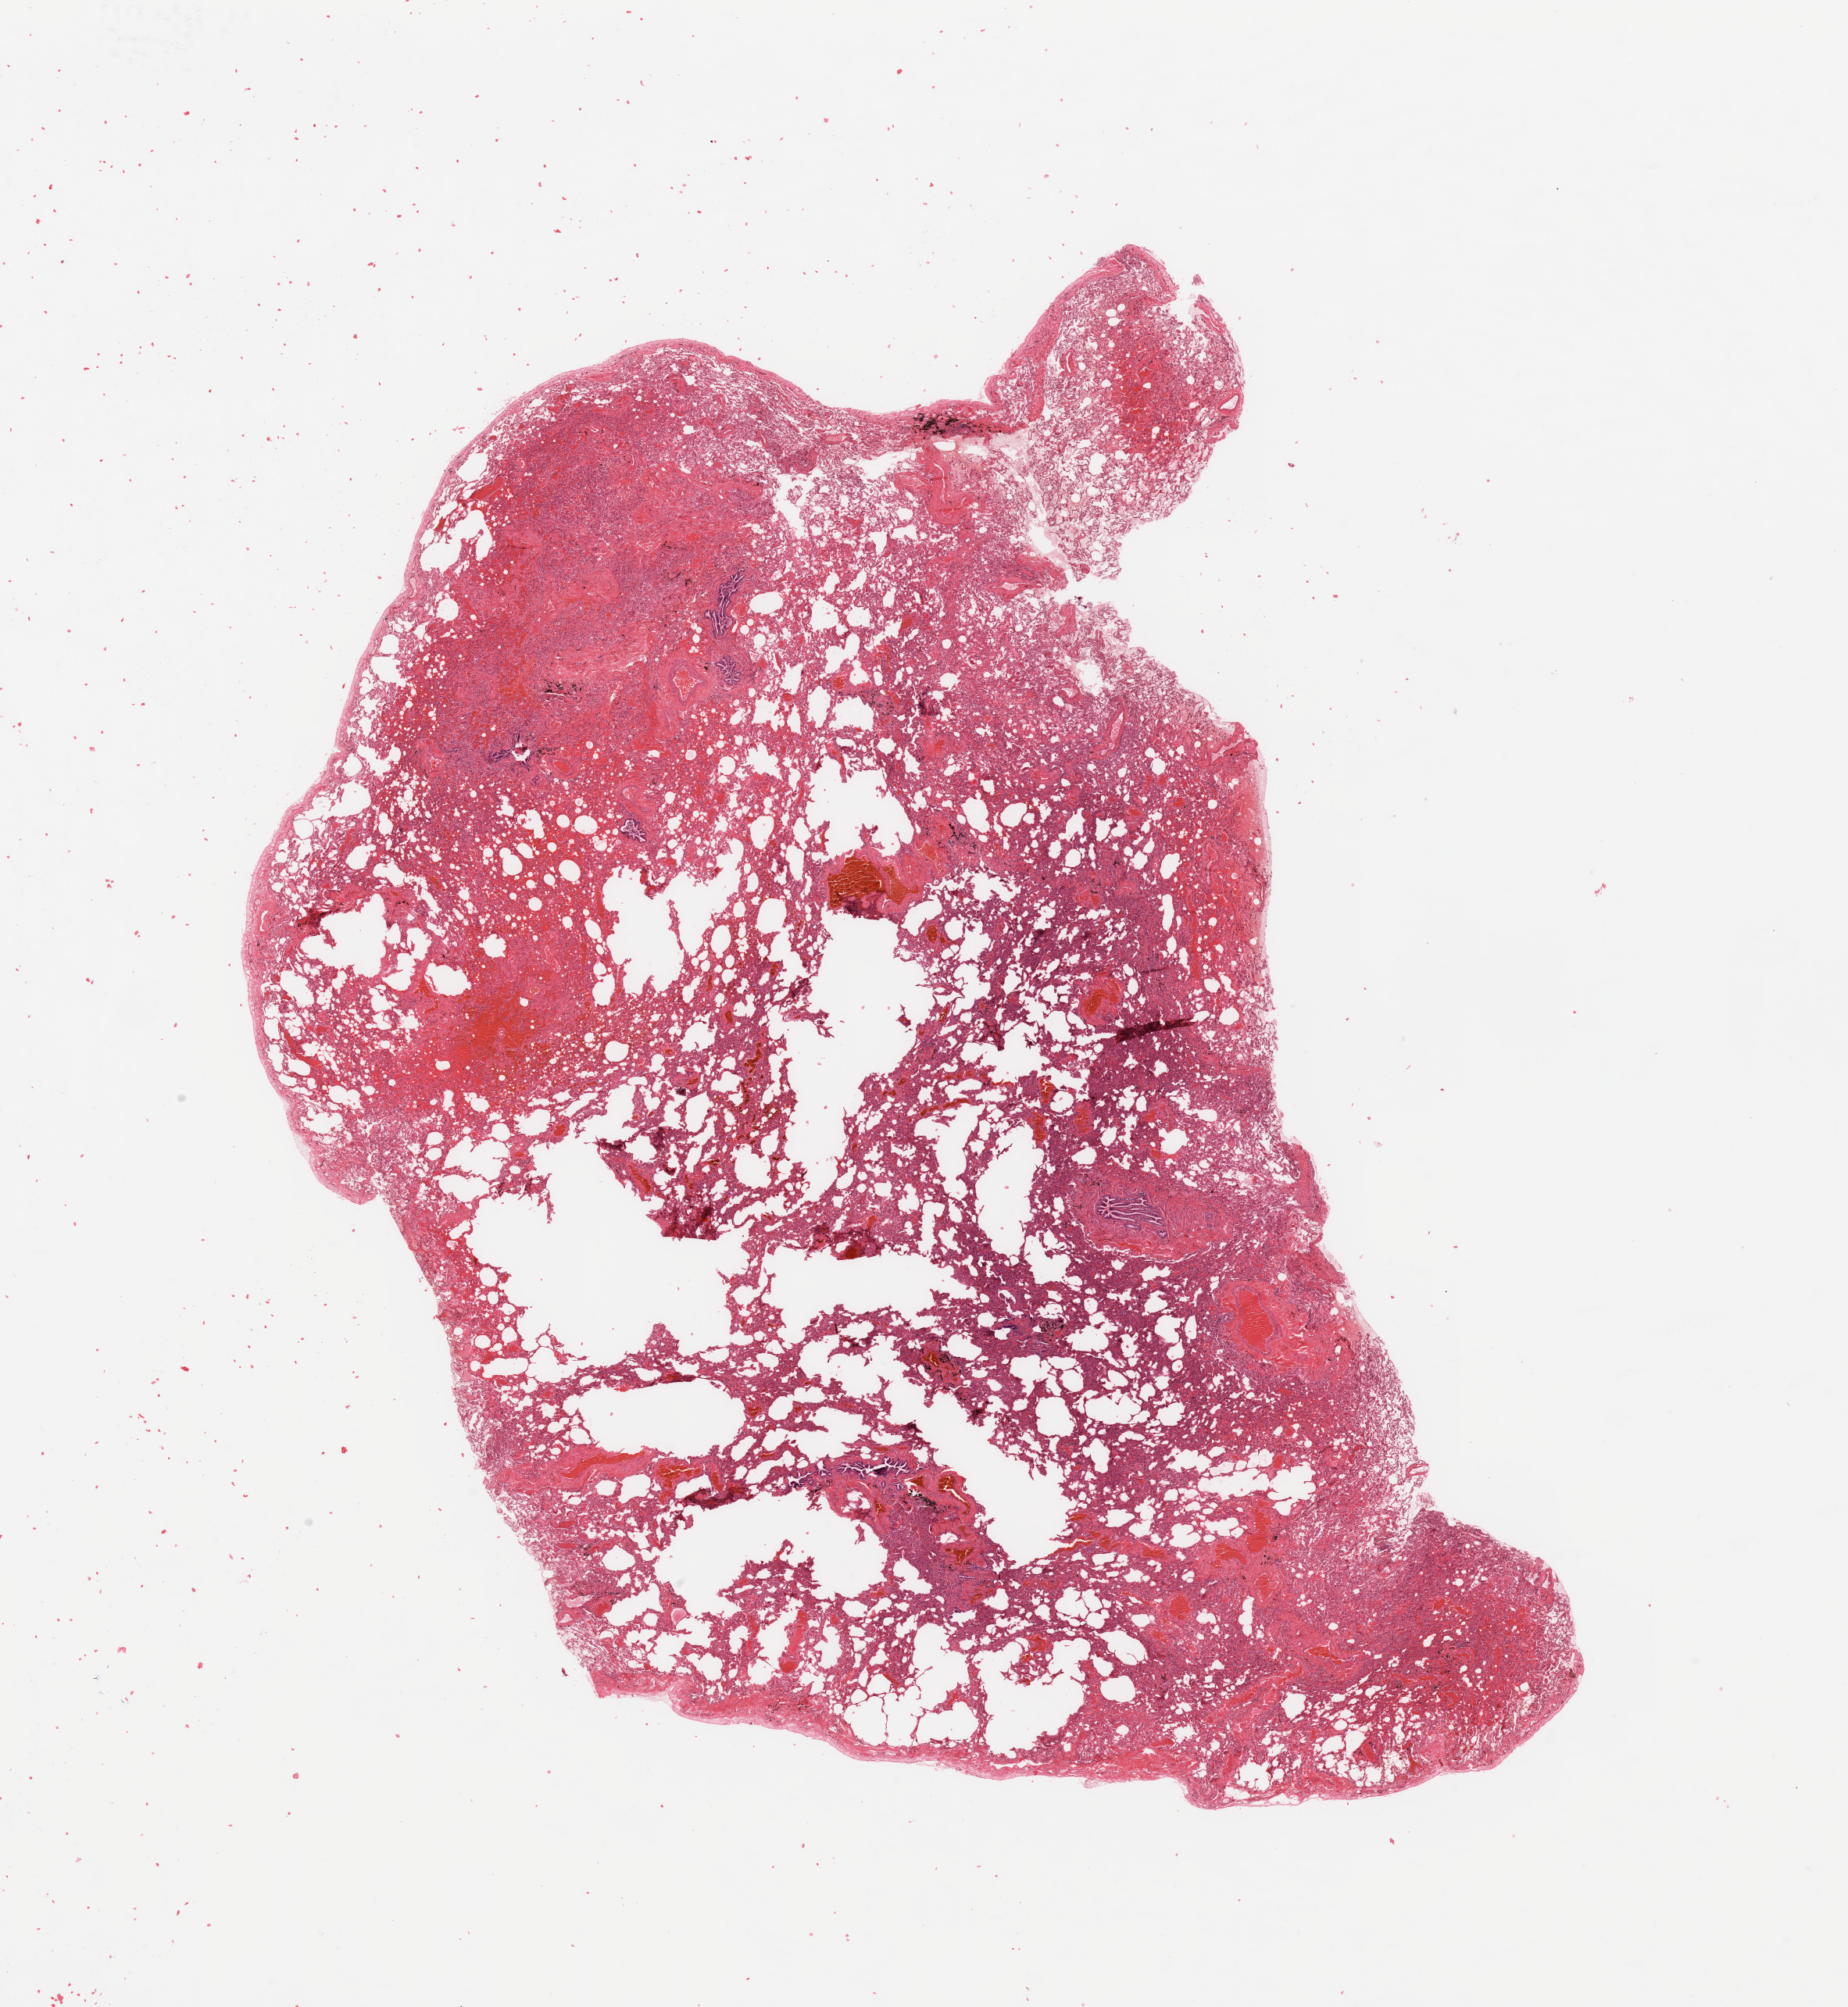
Whole-slide histology image, Hematoxylin and eosin (H&E) stained — a low-resolution overview of the entire scanned area, about 18.7 x 20.3 mm. Normal (non-tumour) tissue sample, sampled site: lung. Patient: female, age 52 years.
- this section: normal (non-tumour) tissue from the same patient
- patient diagnosis: Adenocarcinoma, NOS